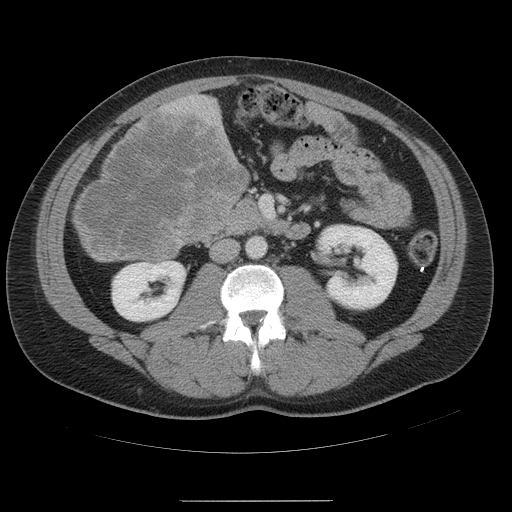
Contrast-enhanced abdominal CT, one axial slice. Position 16 of 54 along the scan axis. Intravenous contrast given. Soft-tissue window (W 400 / L 40 HU). 5 mm slice thickness. 512 × 512 image matrix. Male patient, age 40 years. From the clinical record (not read from this slice): diagnosis: colorectal cancer liver metastases, imaged before liver resection.
Structures marked on this image (expert manual segmentation):
- liver: box from (x=74, y=96) to (x=248, y=263) px
- liver metastasis: (x=74, y=109)–(x=249, y=261)